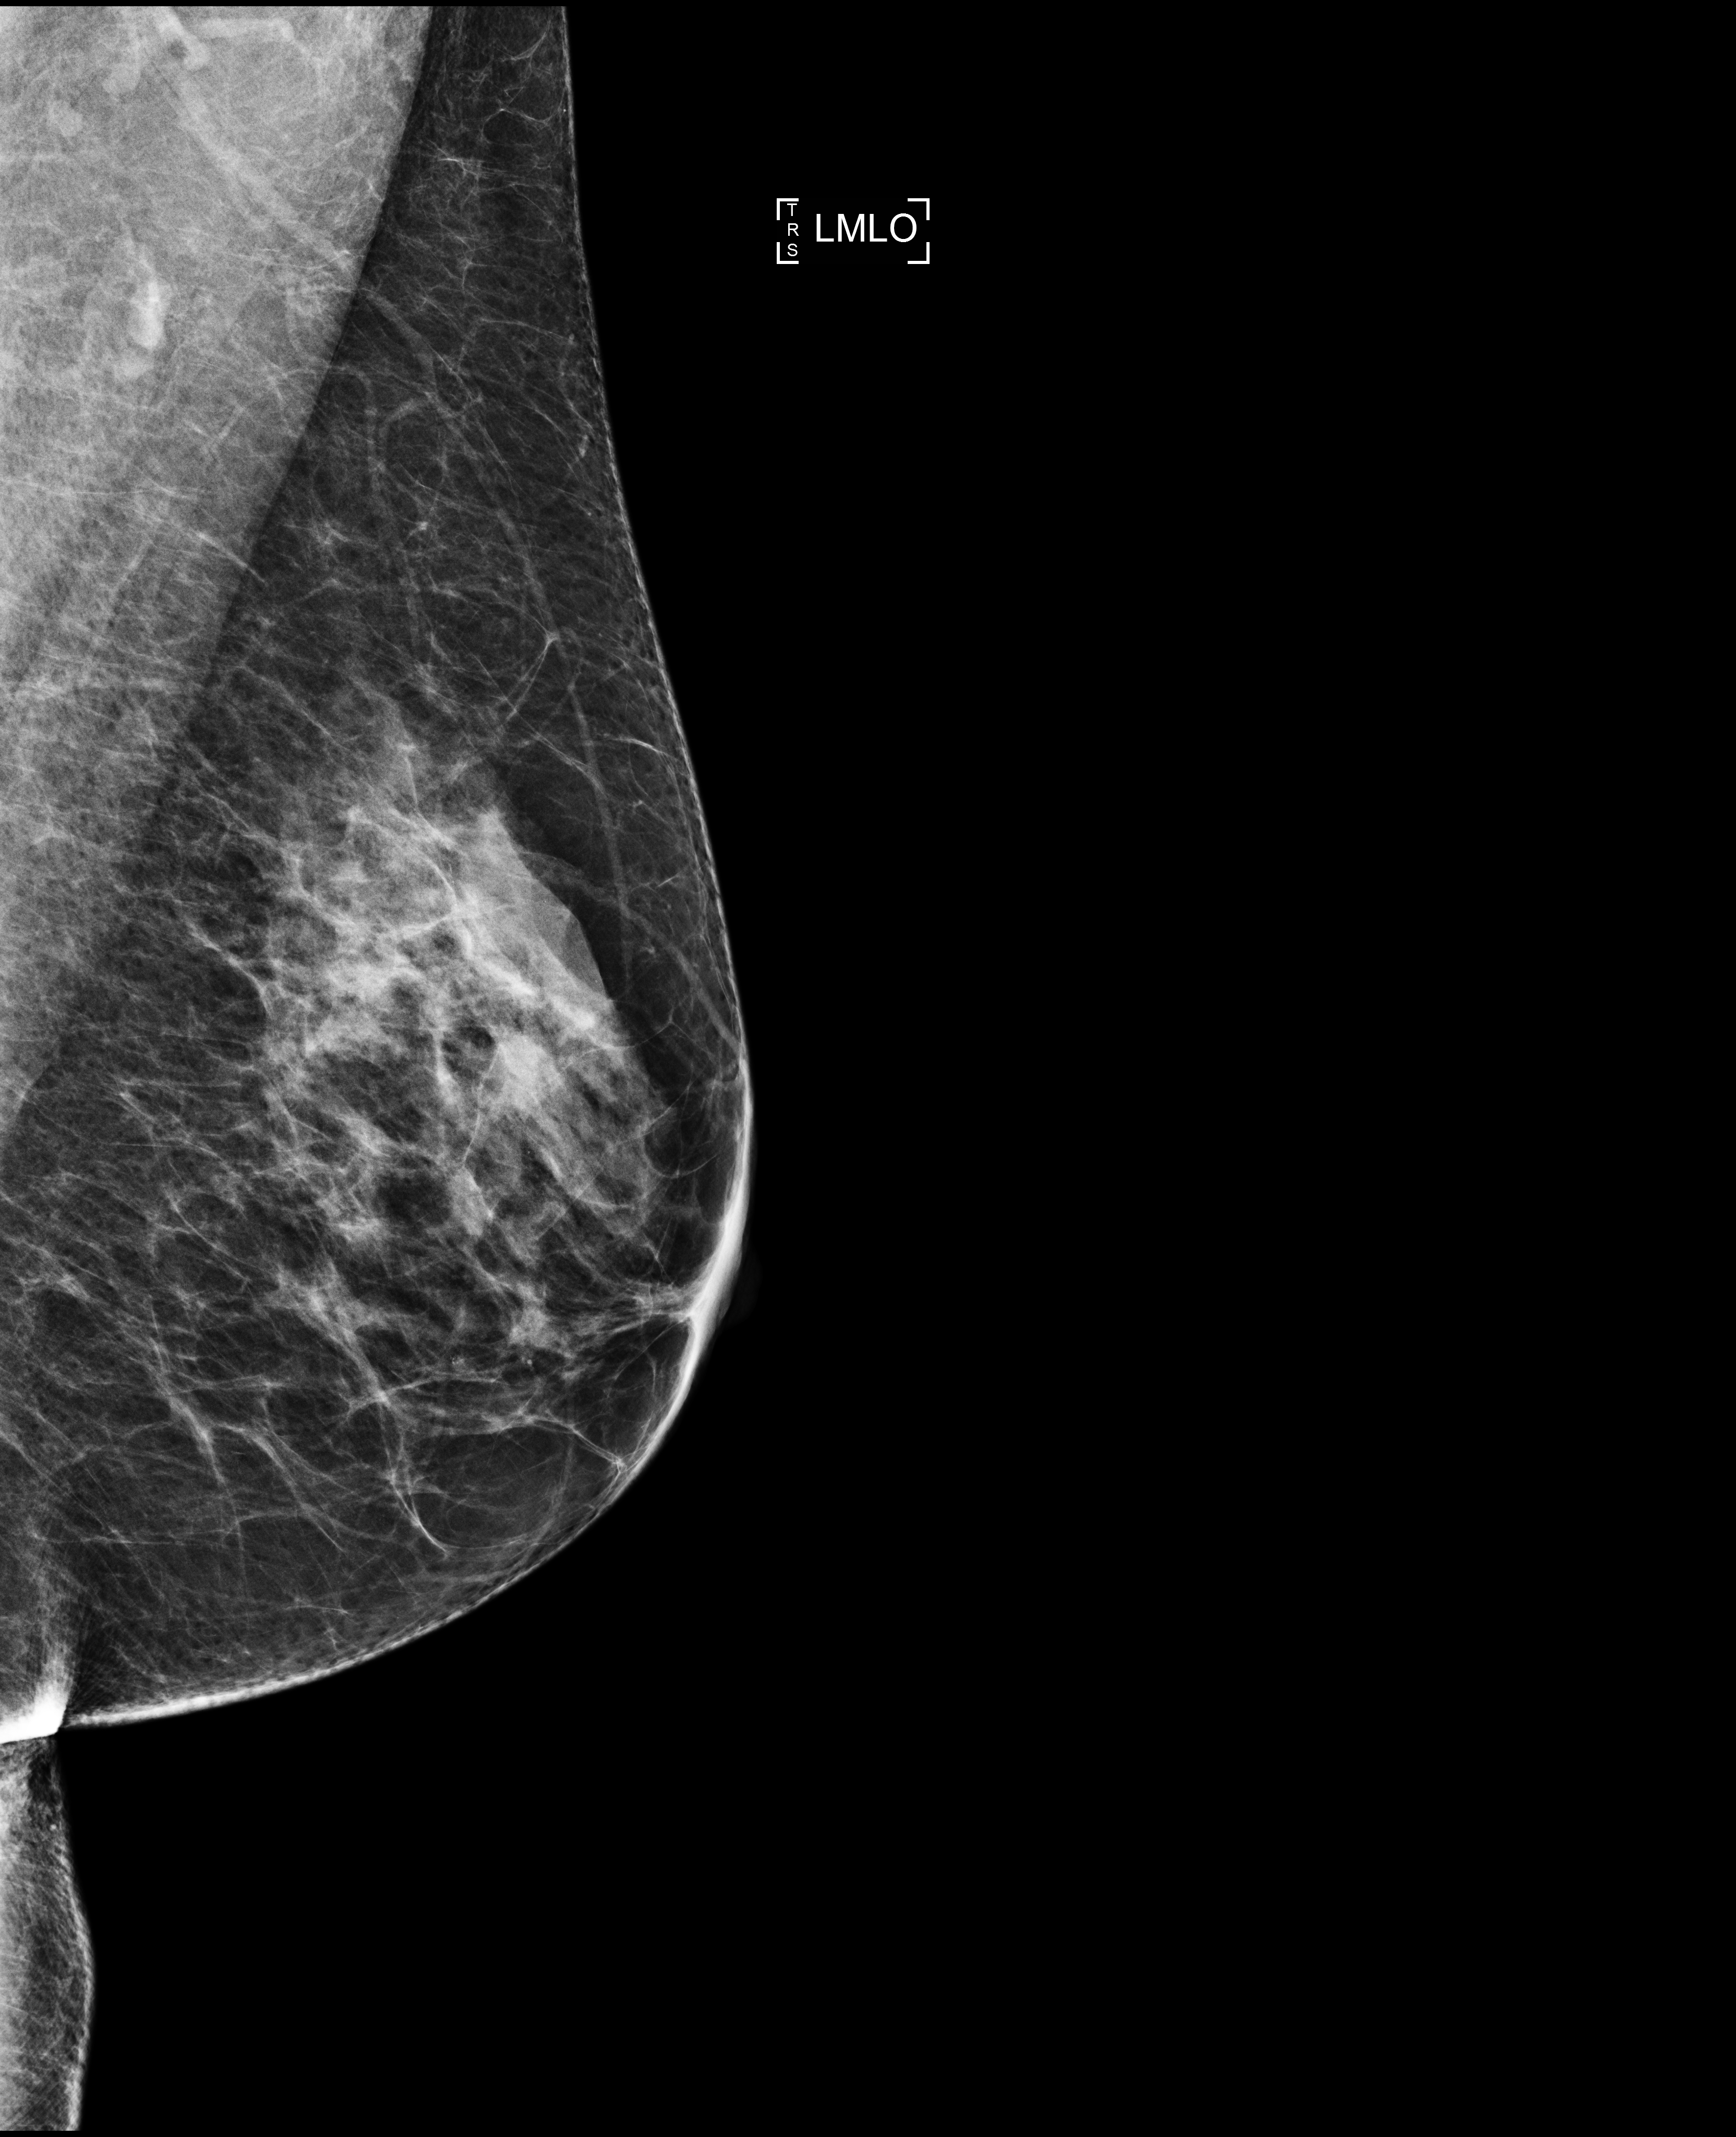
Annual screening mammography examination; compressed breast thickness 62 mm. Female patient, age 64 years.
Image type: full-field digital mammogram. Breast: left. Projection: mediolateral oblique (MLO) view.